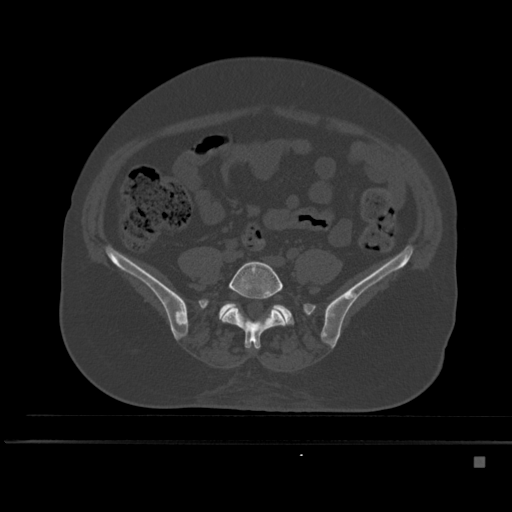
CT including the spine, one axial slice; position 106 of 495 along the scan axis; bone window (W 1800 / L 400 HU); 512 × 512 image matrix, field of view 404 × 404 mm. Patient: female, 33 years. From the clinical record (not read from this slice): primary cancer: breast; vertebrae with lytic lesions (as recorded): T1.
Structures marked on this image (semi-automatic segmentation, software-assisted and operator-edited):
- L5 vertebra: box from (x=220, y=261) to (x=286, y=349) px